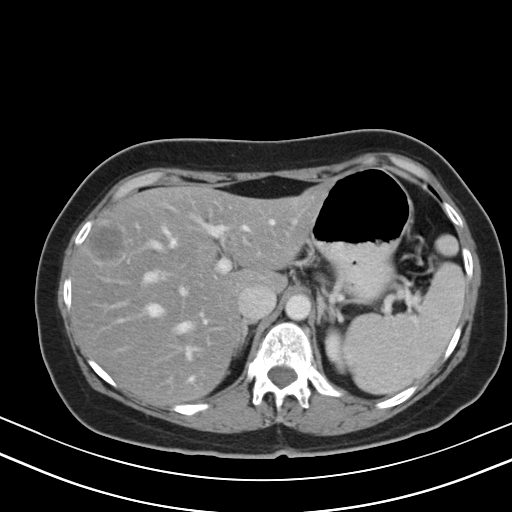
Contrast-enhanced abdominal CT, one axial slice. Slice 33 of 47 in the series (ordered by position). Intravenous contrast given. Soft-tissue window (W 400 / L 40 HU). 5 mm slice thickness. 512 × 512 image matrix, field of view 350 × 350 mm. Female patient. Case-level facts recorded for this patient, not image findings: diagnosis: colorectal cancer liver metastases, imaged before liver resection; multiple liver metastases: no.
Structures marked on this image (manually delineated by an expert):
- hepatic veins: bounding box <120,219,274,381> (left, top, right, bottom; pixels)
- liver: <74,189,323,400>
- planned liver remnant (the part of the liver to remain after resection): <74,189,324,400>
- portal vein (with intrahepatic branches): <111,218,231,357>
- liver metastasis: <89,224,125,262>